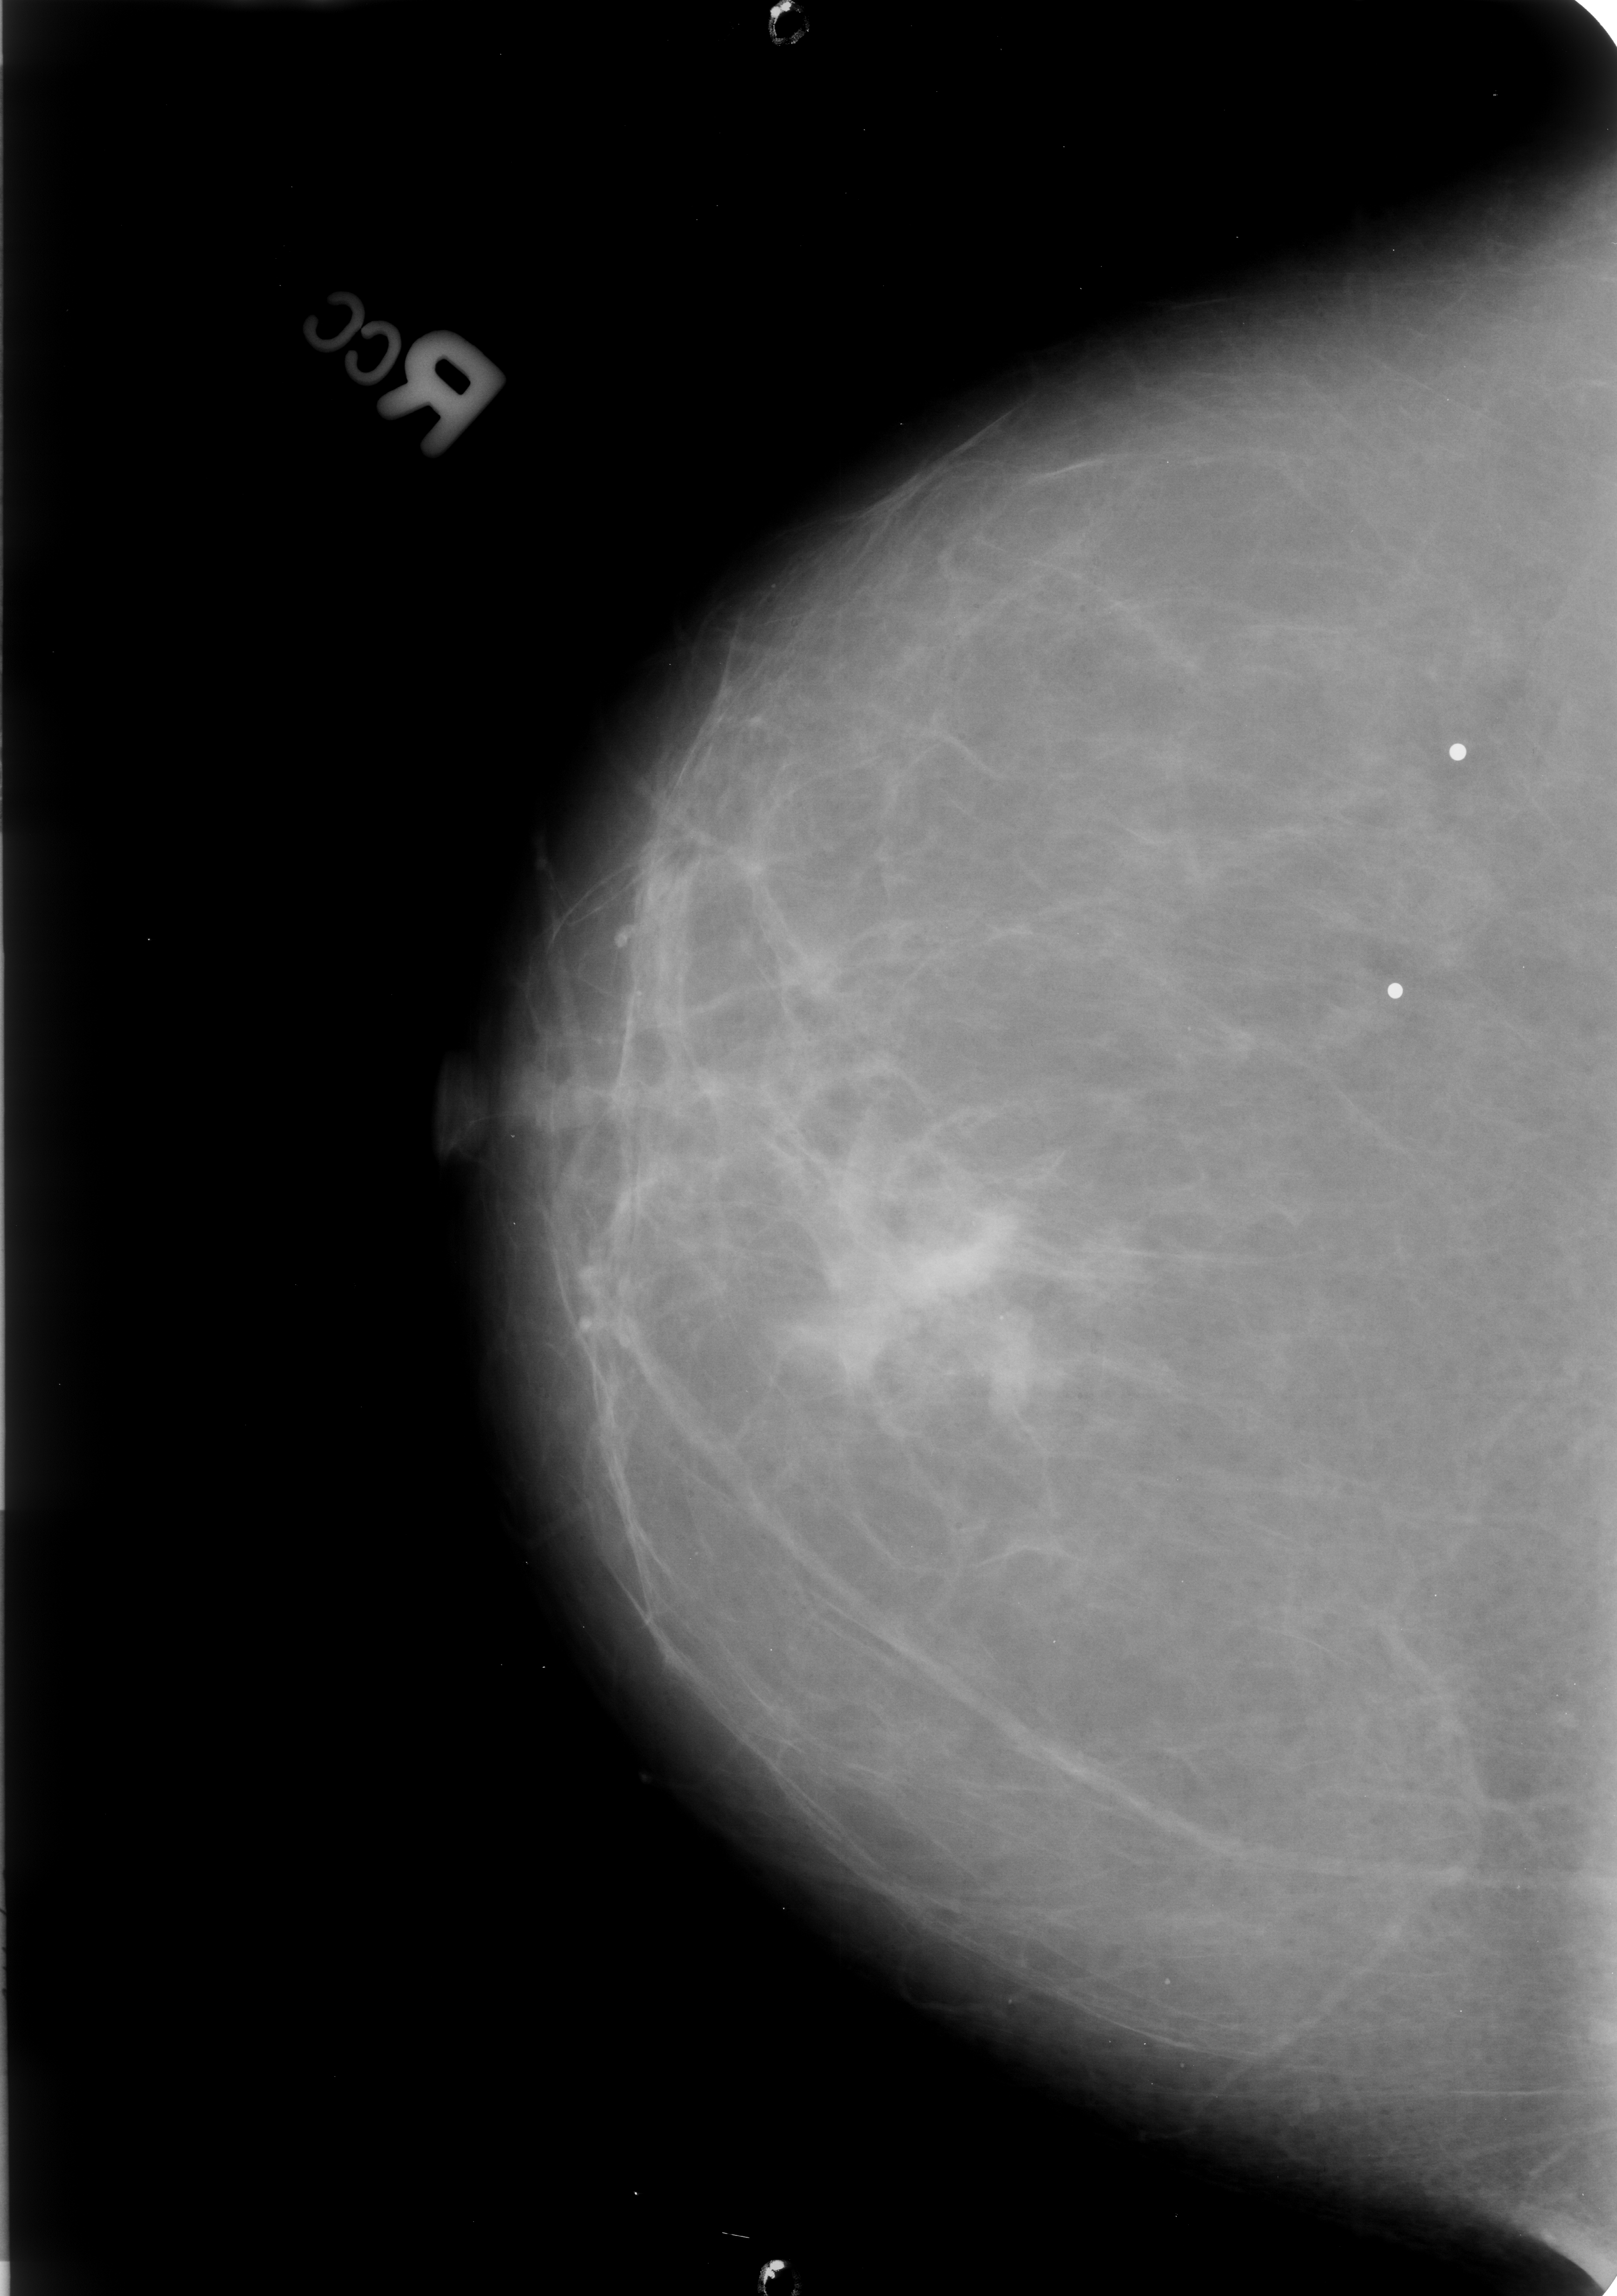
Digitized screen-film mammogram, right breast, craniocaudal (CC) view, breast composition: almost entirely fatty (BI-RADS density category 1 of 4).
Finding: mass, shape irregular / architectural distortion, margins ill defined / spiculated; BI-RADS assessment category 4; pathology (as recorded): malignant.